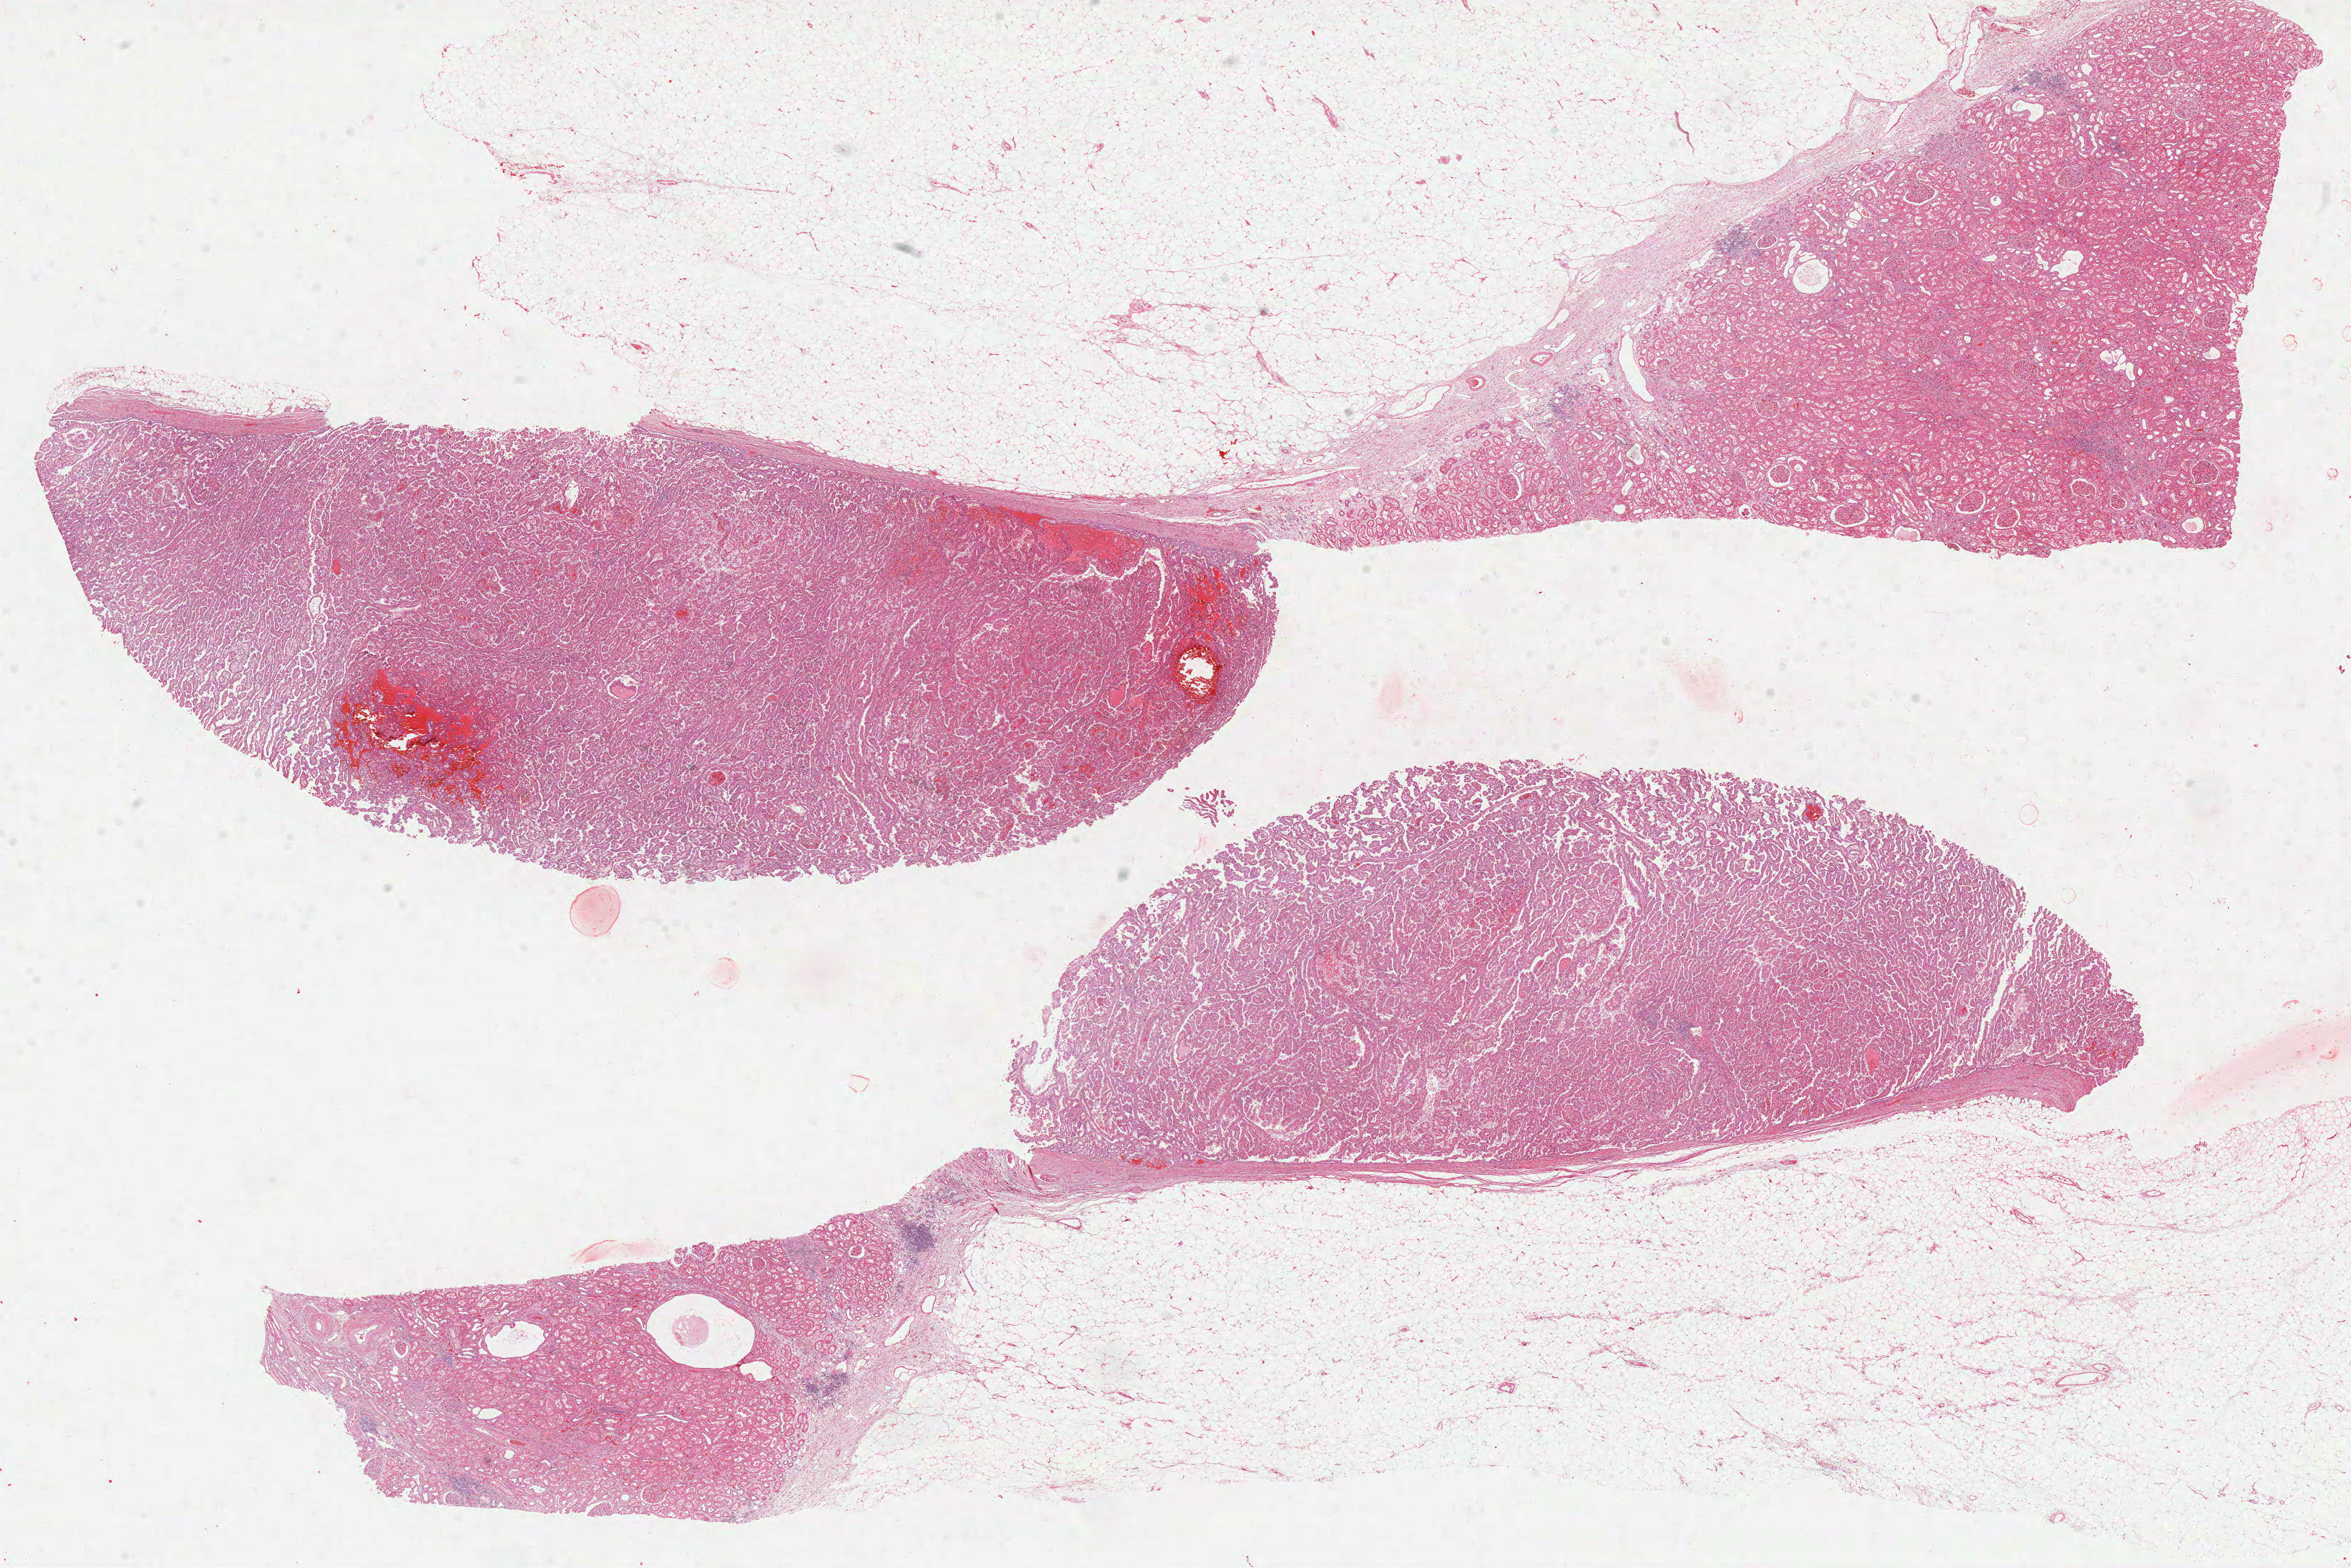
Digitized H&E tissue section (whole slide), shown as a low-resolution overview of the whole scanned area (about 26.3 x 17.6 mm). Formalin-fixed paraffin-embedded (FFPE) diagnostic section. Sample: primary tumour, kidney. Male, age 56 years at initial diagnosis.
Pathologic diagnosis: Papillary adenocarcinoma, NOS. AJCC pathologic stage: I. Lymph nodes positive (case pathology): 0 of 2 examined.